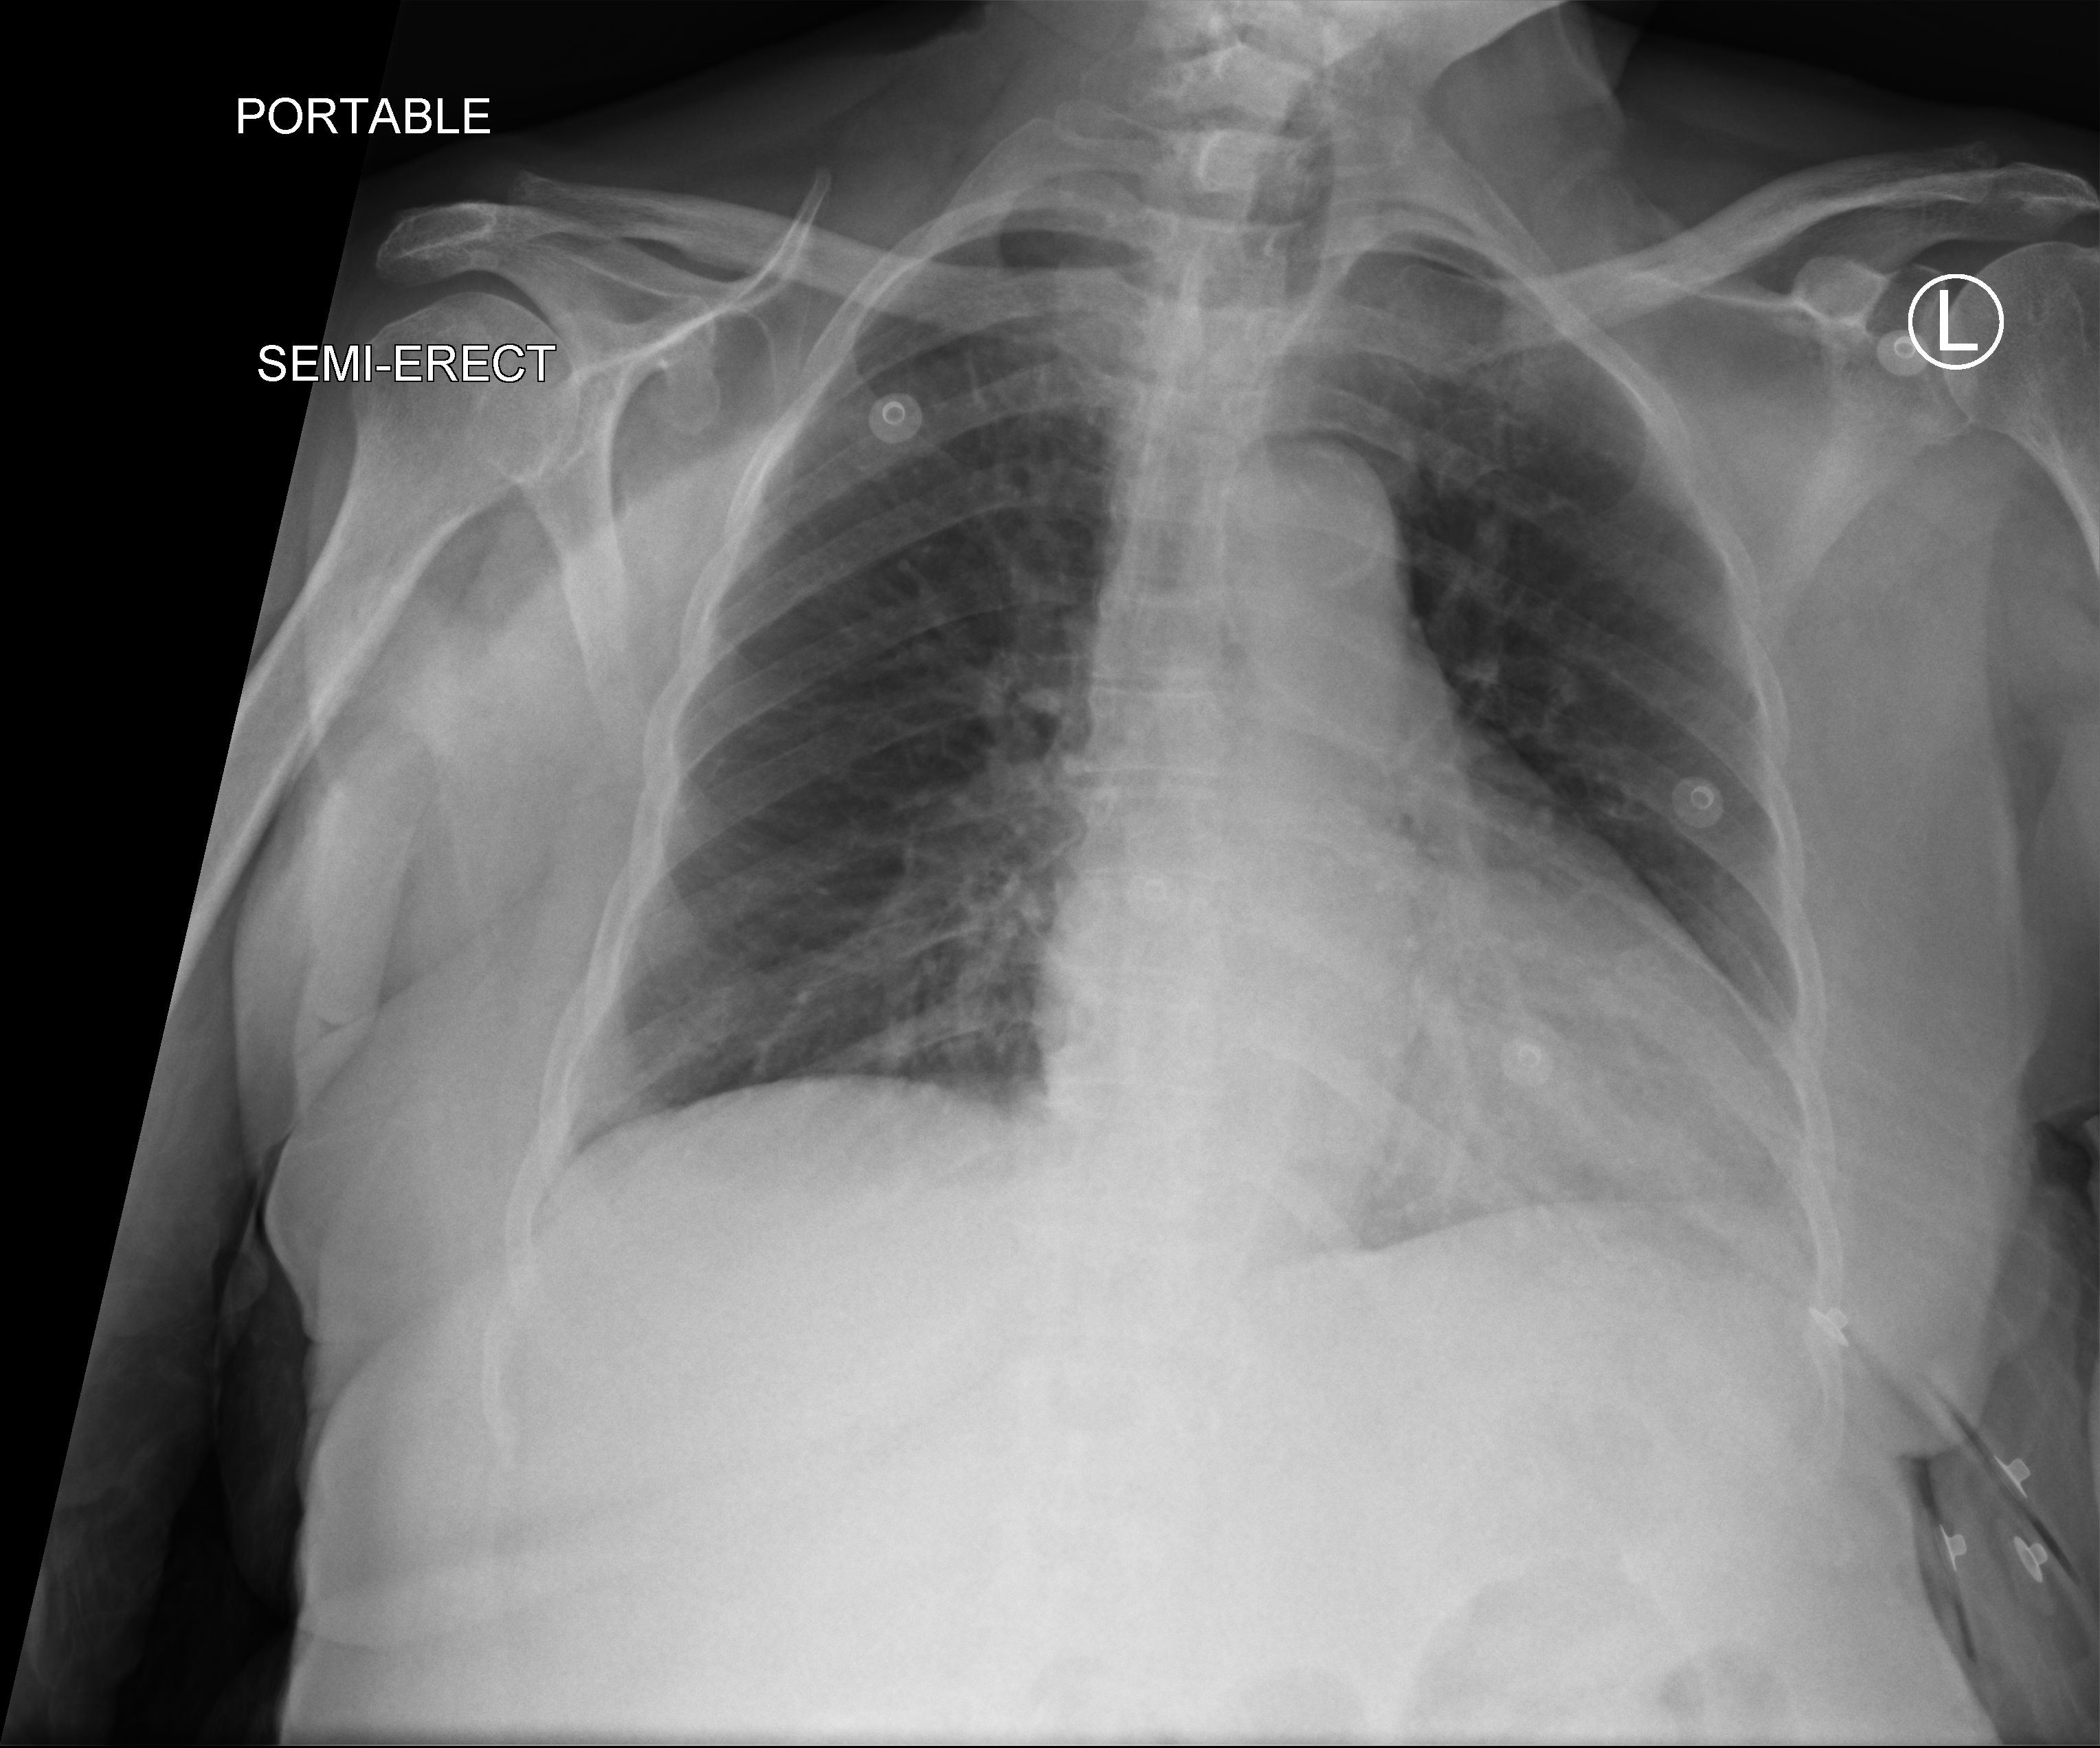
Bedside chest radiograph (computed radiography), anteroposterior (AP) projection. Patient hospitalised with COVID-19; female, aged 75–90 years.
Admission-level facts for this patient (not findings on this image; timing relative to this image not recorded): hypertension (admission record): yes; mechanically ventilated during this hospital stay: no.